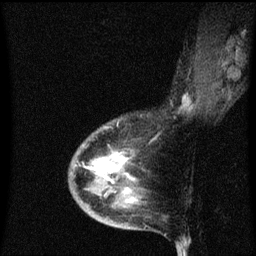
Breast MRI (dynamic contrast-enhanced), one sagittal slice. Slice 25 of 60 in the series (ordered by position). Dynamic contrast-enhanced series, image 2 of 3 at this slice position (ordered by acquisition). 1.5 T. TE 4.2 ms, TR 8.4 ms. 256 × 256 image matrix. Patient: female, 38 years. From the clinical record (not read from this slice): setting: breast cancer imaged before/during neoadjuvant chemotherapy; receptor status: HR-positive, HER2-negative.
Outlined on this slice (semi-automatic segmentation, software-assisted and operator-edited):
- analysis volume of interest (the breast-tissue region the enhancement analysis was run in; not a lesion): bounding box <70,126,143,205> (left, top, right, bottom; pixels)
- tumour enhancement mask (voxels above the 70 % enhancement threshold inside the analysis volume of interest): <94,152,127,193>